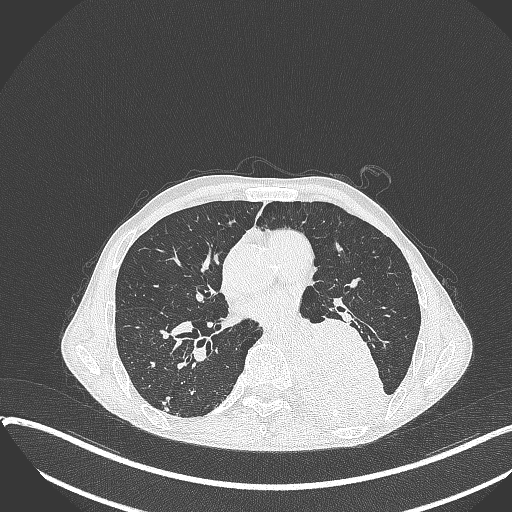
Chest CT, one axial slice; slice 182 of 401 in the series (ordered by position); reconstruction kernel B70f; lung window (W 1500 / L -600 HU); 1 mm slice thickness; 512 × 512 image matrix. Patient: male, 57 years. From the clinical record (not read from this slice): clinical TNM (as recorded): T4 N0 M0.
Structures marked on this image (rectangle marked by the reading radiologist):
- lung tumour (recorded histology: squamous cell carcinoma): bounding box <295,315,388,430> (left, top, right, bottom; pixels)